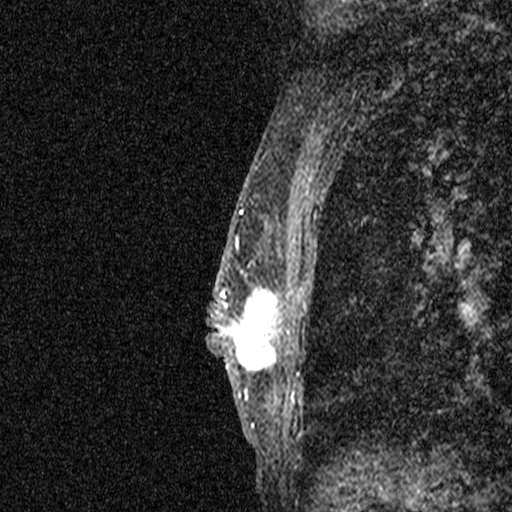
Breast MRI (dynamic contrast-enhanced), one sagittal slice; dynamic contrast-enhanced study with each time point stored as its own series, time point 2 of 3 at this slice position (early post-contrast, ordered by acquisition time); 1.5 T; TE 4.5 ms, TR 11 ms; 2.05 mm slice thickness; 512 × 512 image matrix, field of view 200 × 200 mm. Patient: female, 44 years. Case-level facts recorded for this patient, not image findings: setting: breast cancer imaged before/during neoadjuvant chemotherapy; receptor status: HR-positive, HER2-negative.
Annotated regions visible in this slice (semi-automatically segmented with operator editing):
- analysis volume of interest (the breast-tissue region the enhancement analysis was run in; not a lesion): bounding box [x1, y1, x2, y2] px = [204, 254, 280, 401]
- tumour enhancement mask (voxels above the 90 % enhancement threshold inside the analysis volume of interest): [208, 254, 280, 395]